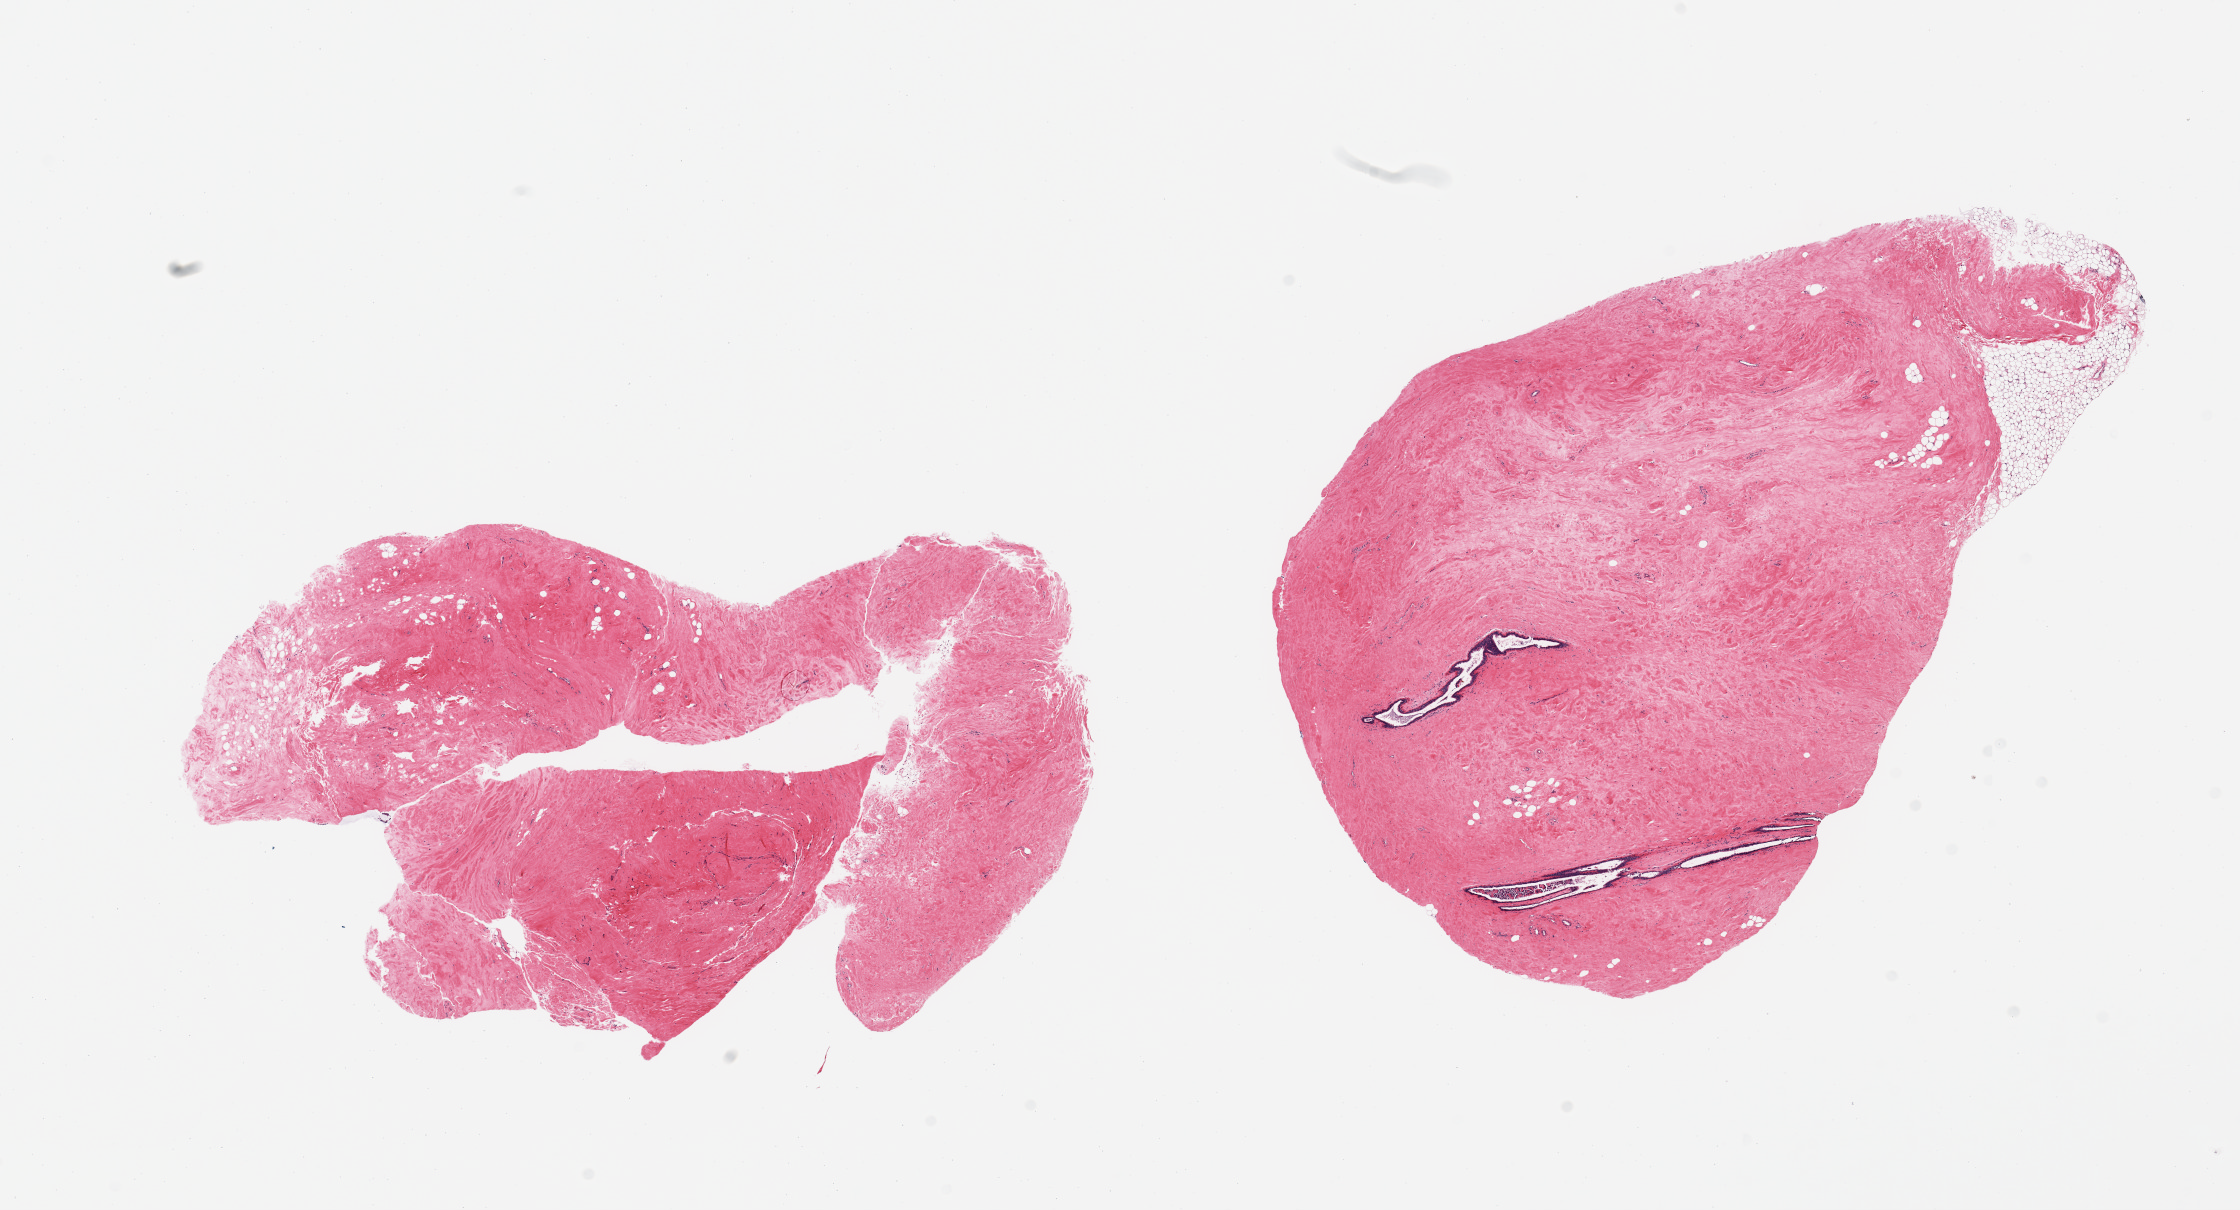
Haematoxylin and eosin whole-slide image, whole scanned area (about 17.7 x 9.6 mm, acquisition: 20x scan) shown as a low-resolution overview. PAXgene-fixed paraffin-embedded (PFPE) section. Section of breast (target tissue). Donor tissue sample. Donor: male.
Reviewer comment on this tissue sample: 2 pieces, prominent gynecolmastoid stromal and ductal hyerplasia; ductal elements.